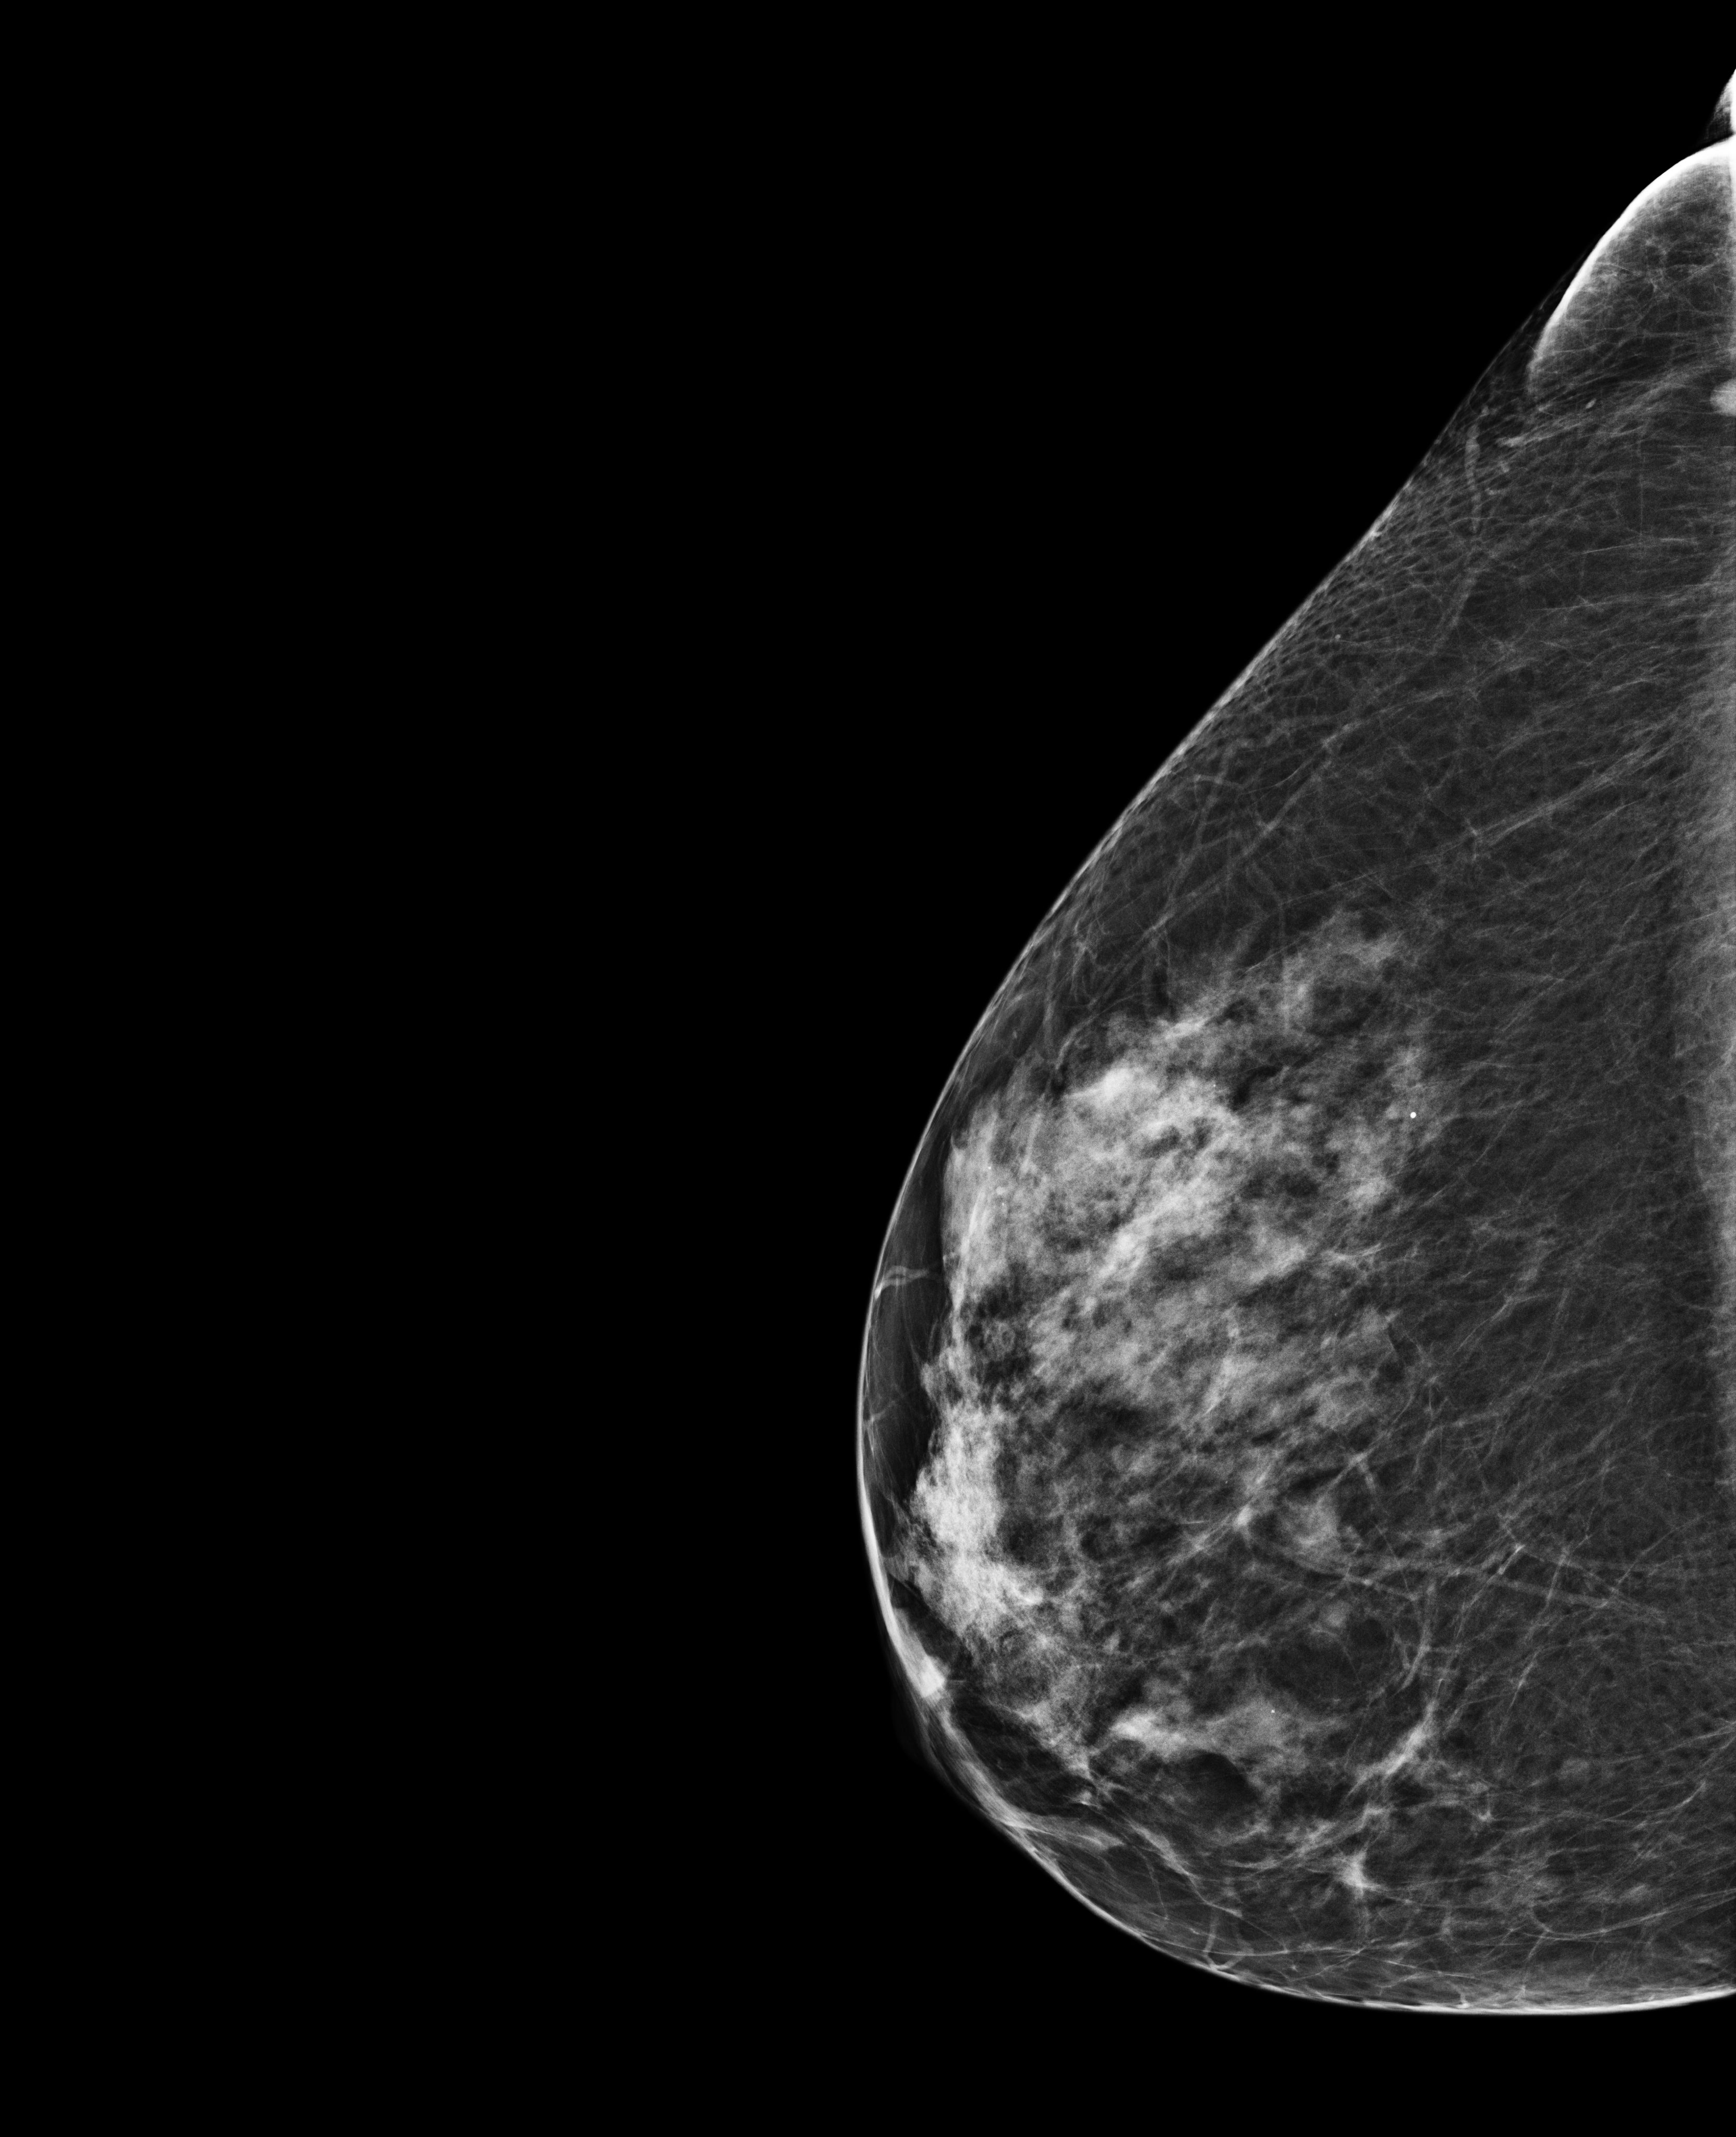
Full-field digital mammogram (FFDM), right breast, exaggerated CC view (lateral), annual screening mammography examination, compressed breast thickness 52 mm, system: Selenia Dimensions. Patient aged 63 years (female).
Final BI-RADS category for the screening round (tomosynthesis exam, both breasts): category 1.